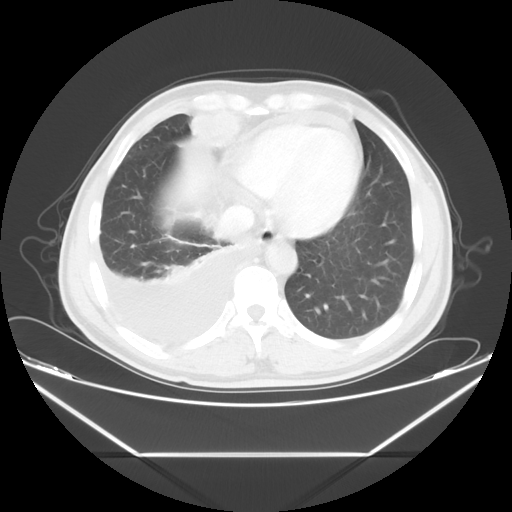
Chest CT, one axial slice; slice 15 of 56 in the series (ordered by position); reconstruction kernel STANDARD; 120 kVp; lung window (W 1500 / L -600 HU); 512 × 512 image matrix, field of view 412 × 412 mm. Patient: male, 57 years. From the clinical record (not read from this slice): clinical TNM (as recorded): T2 N3 M1.
Structures marked on this image (rectangle marked by the reading radiologist):
- lung tumour (recorded histology: adenocarcinoma): bounding box [x1, y1, x2, y2] px = [189, 106, 255, 150]